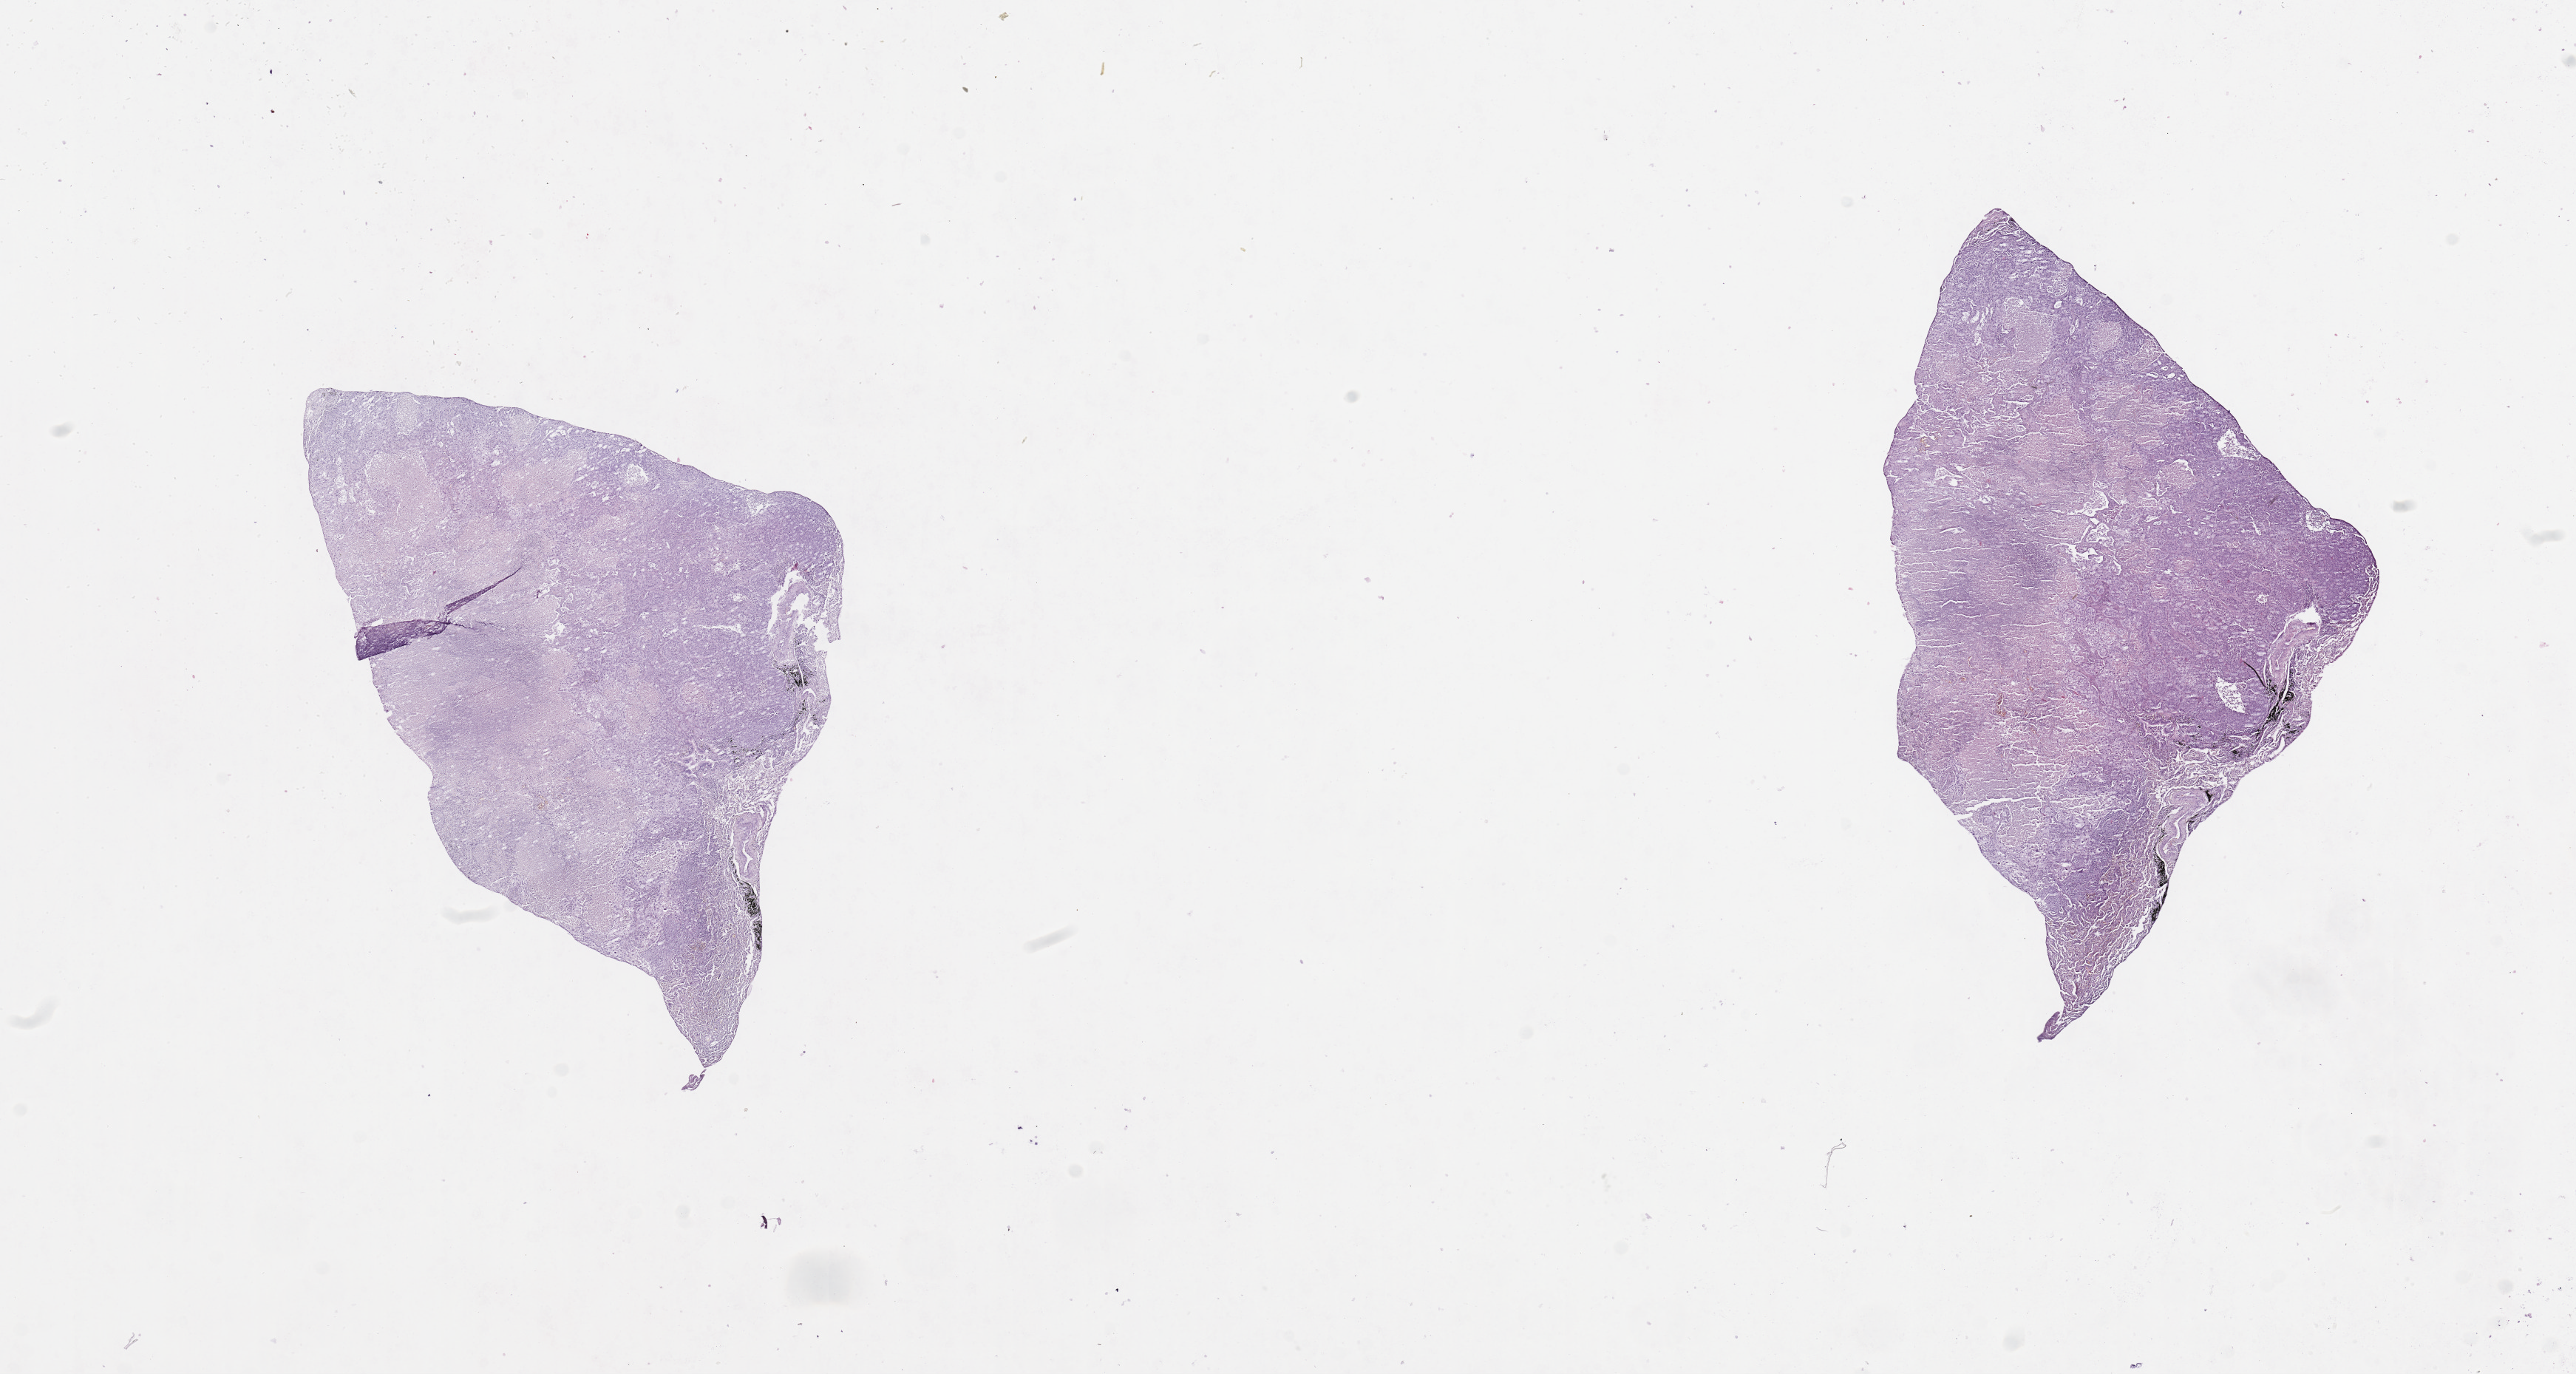
Digitized Hematoxylin and eosin (H&E) stained tissue section (whole slide), shown as a low-resolution overview of the whole scanned area (about 27.6 x 14.7 mm, from a 20x scan). Tumour tissue sample, lung. Patient: male, age 74 years. Histologic grade: G2 (moderately differentiated).
* AJCC pathologic stage: IIIA
* primary tumour site (as recorded): left lower lobe
* histologic diagnosis: Squamous cell carcinoma, NOS